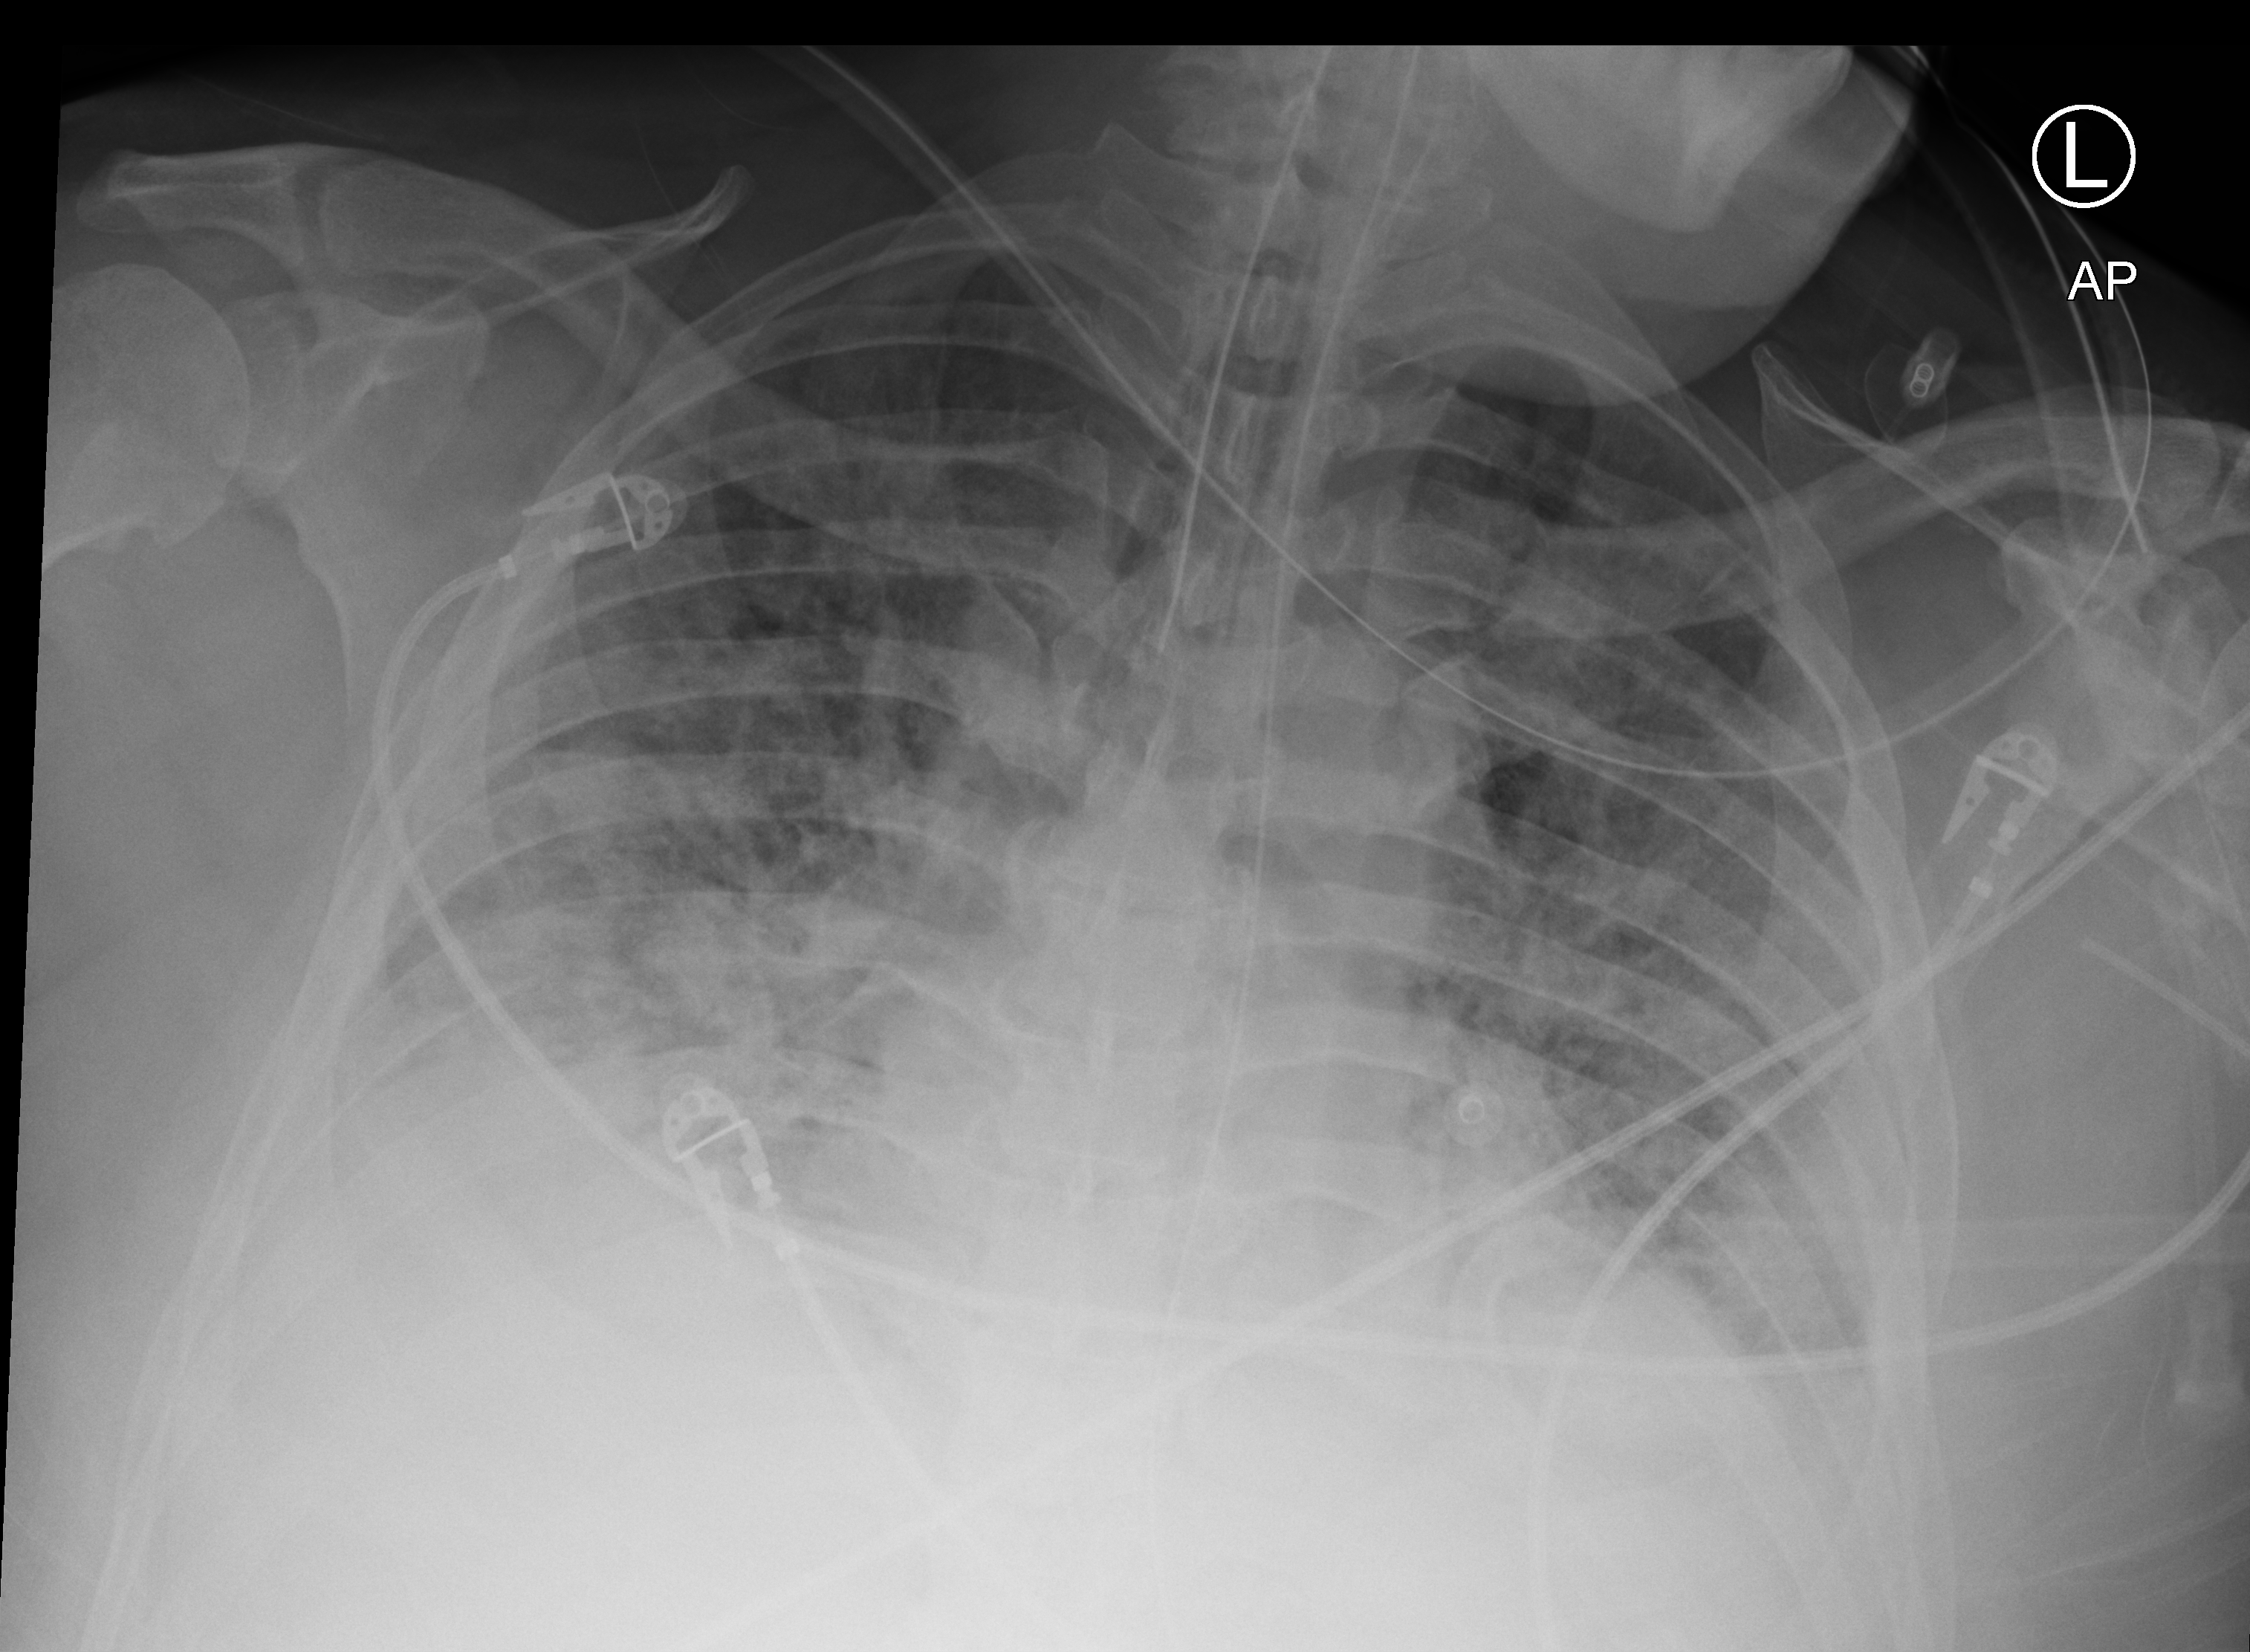
Chest X-ray (portable). Male patient hospitalised with COVID-19, age 18–59 years.
Admission-level facts for this patient (not findings on this image; timing relative to this image not recorded): admitted to intensive care during this hospital stay: yes.